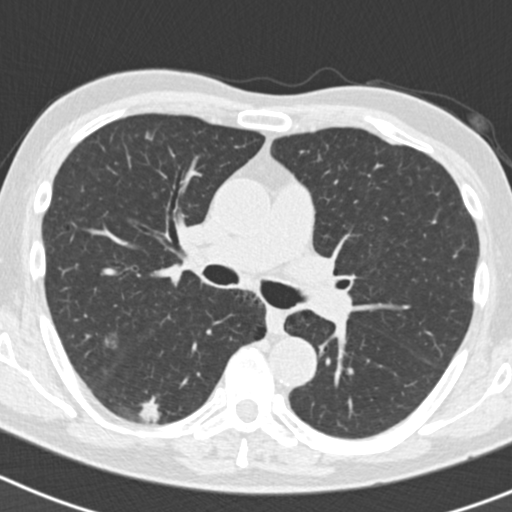
Axial slice from a low-dose chest CT screening exam, second screening round (one year after baseline), lung window (W 1500 / L -600 HU), 2 mm slice thickness, 120 kVp, slice 70 of 186 in the series. Male participant, aged 70 years at enrolment. Current smoker at enrolment.
Lesion marked by an expert reader, bounding box (x1, y1, x2, y2) in pixels: (135, 381, 194, 435). The screening reader recorded 5 non-calcified nodules or masses ≥4 mm on this exam (right lower lobe, right lower lobe, right upper lobe, right upper lobe, left upper lobe); which of them this box marks is not recorded. Official screen result: positive, other. Lung cancer was diagnosed 622 days after this screen: bronchiolo-alveolar adenocarcinoma, NOS, right lower lobe, poorly differentiated (G3), stage IB (AJCC 6th edition), 30 mm at pathology.